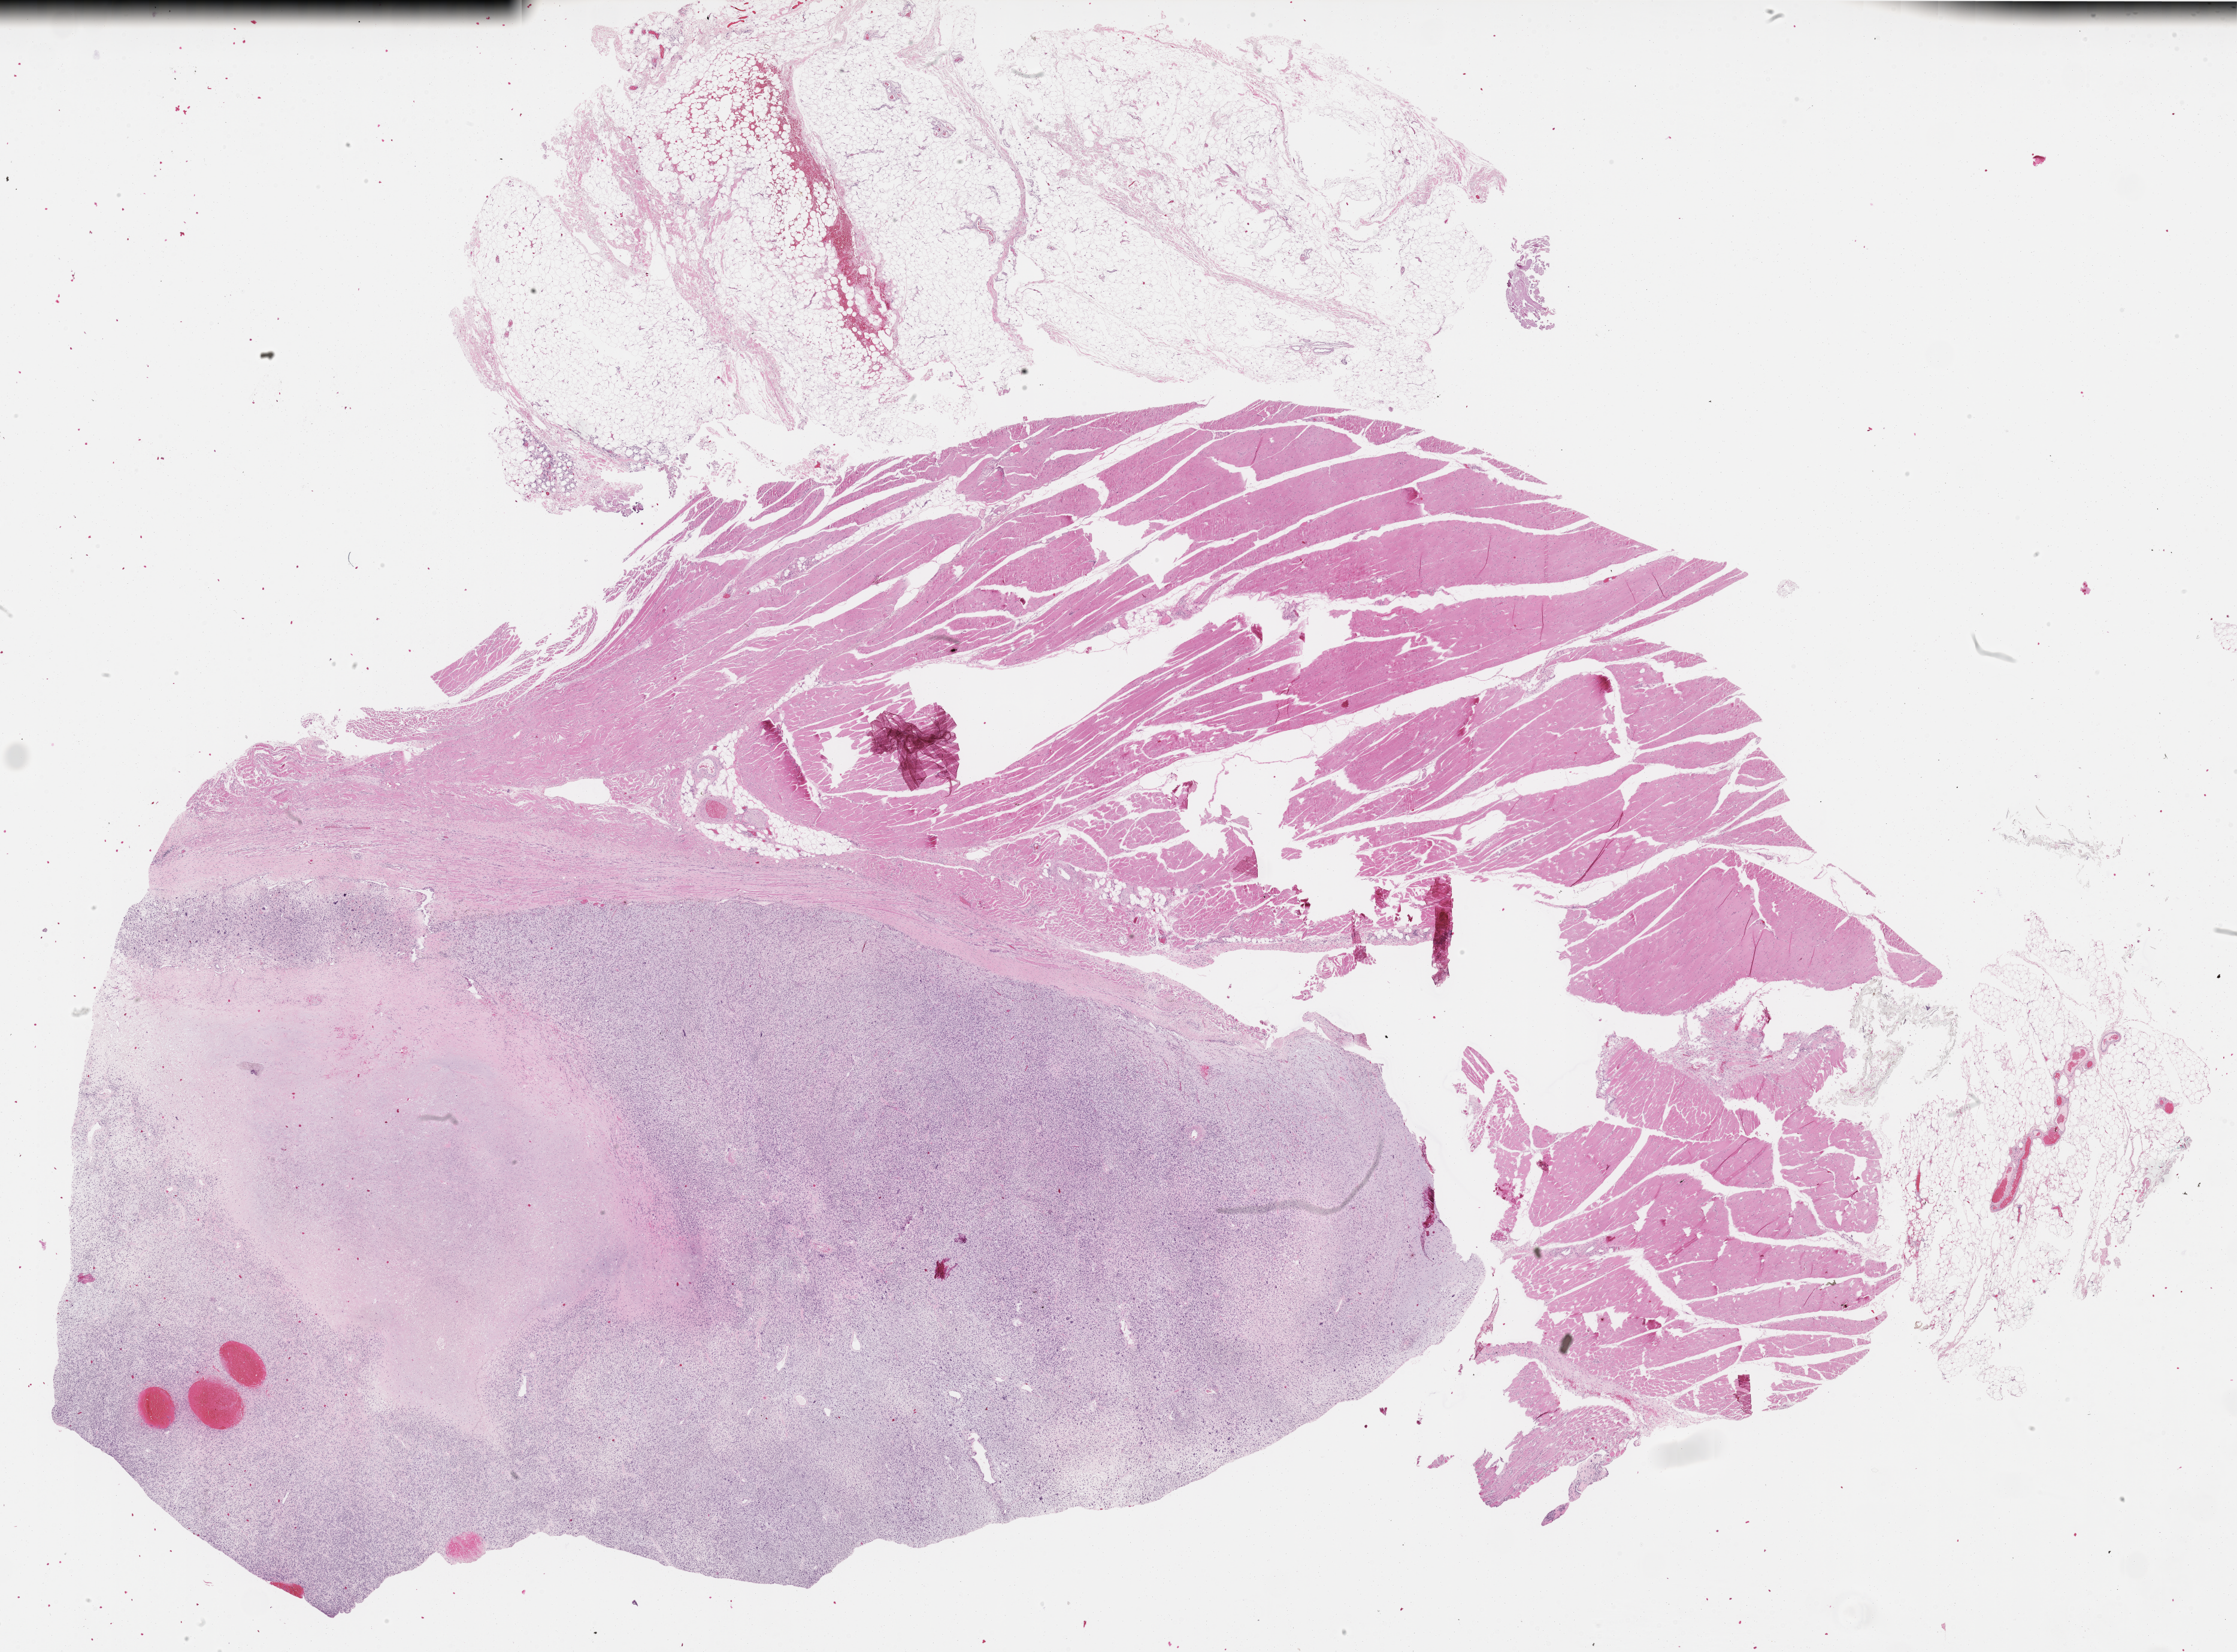
Whole-slide histology image, H&E-stained — low-resolution overview of the scanned area, about 30.2 x 22.3 mm (from a 40x scan); FFPE section; sample: primary tumour, connective, subcutaneous and other soft tissues. Female patient; age at initial diagnosis 50 years.
* pathologic diagnosis: Fibromyxosarcoma (connective, subcutaneous and other soft tissues of thorax)